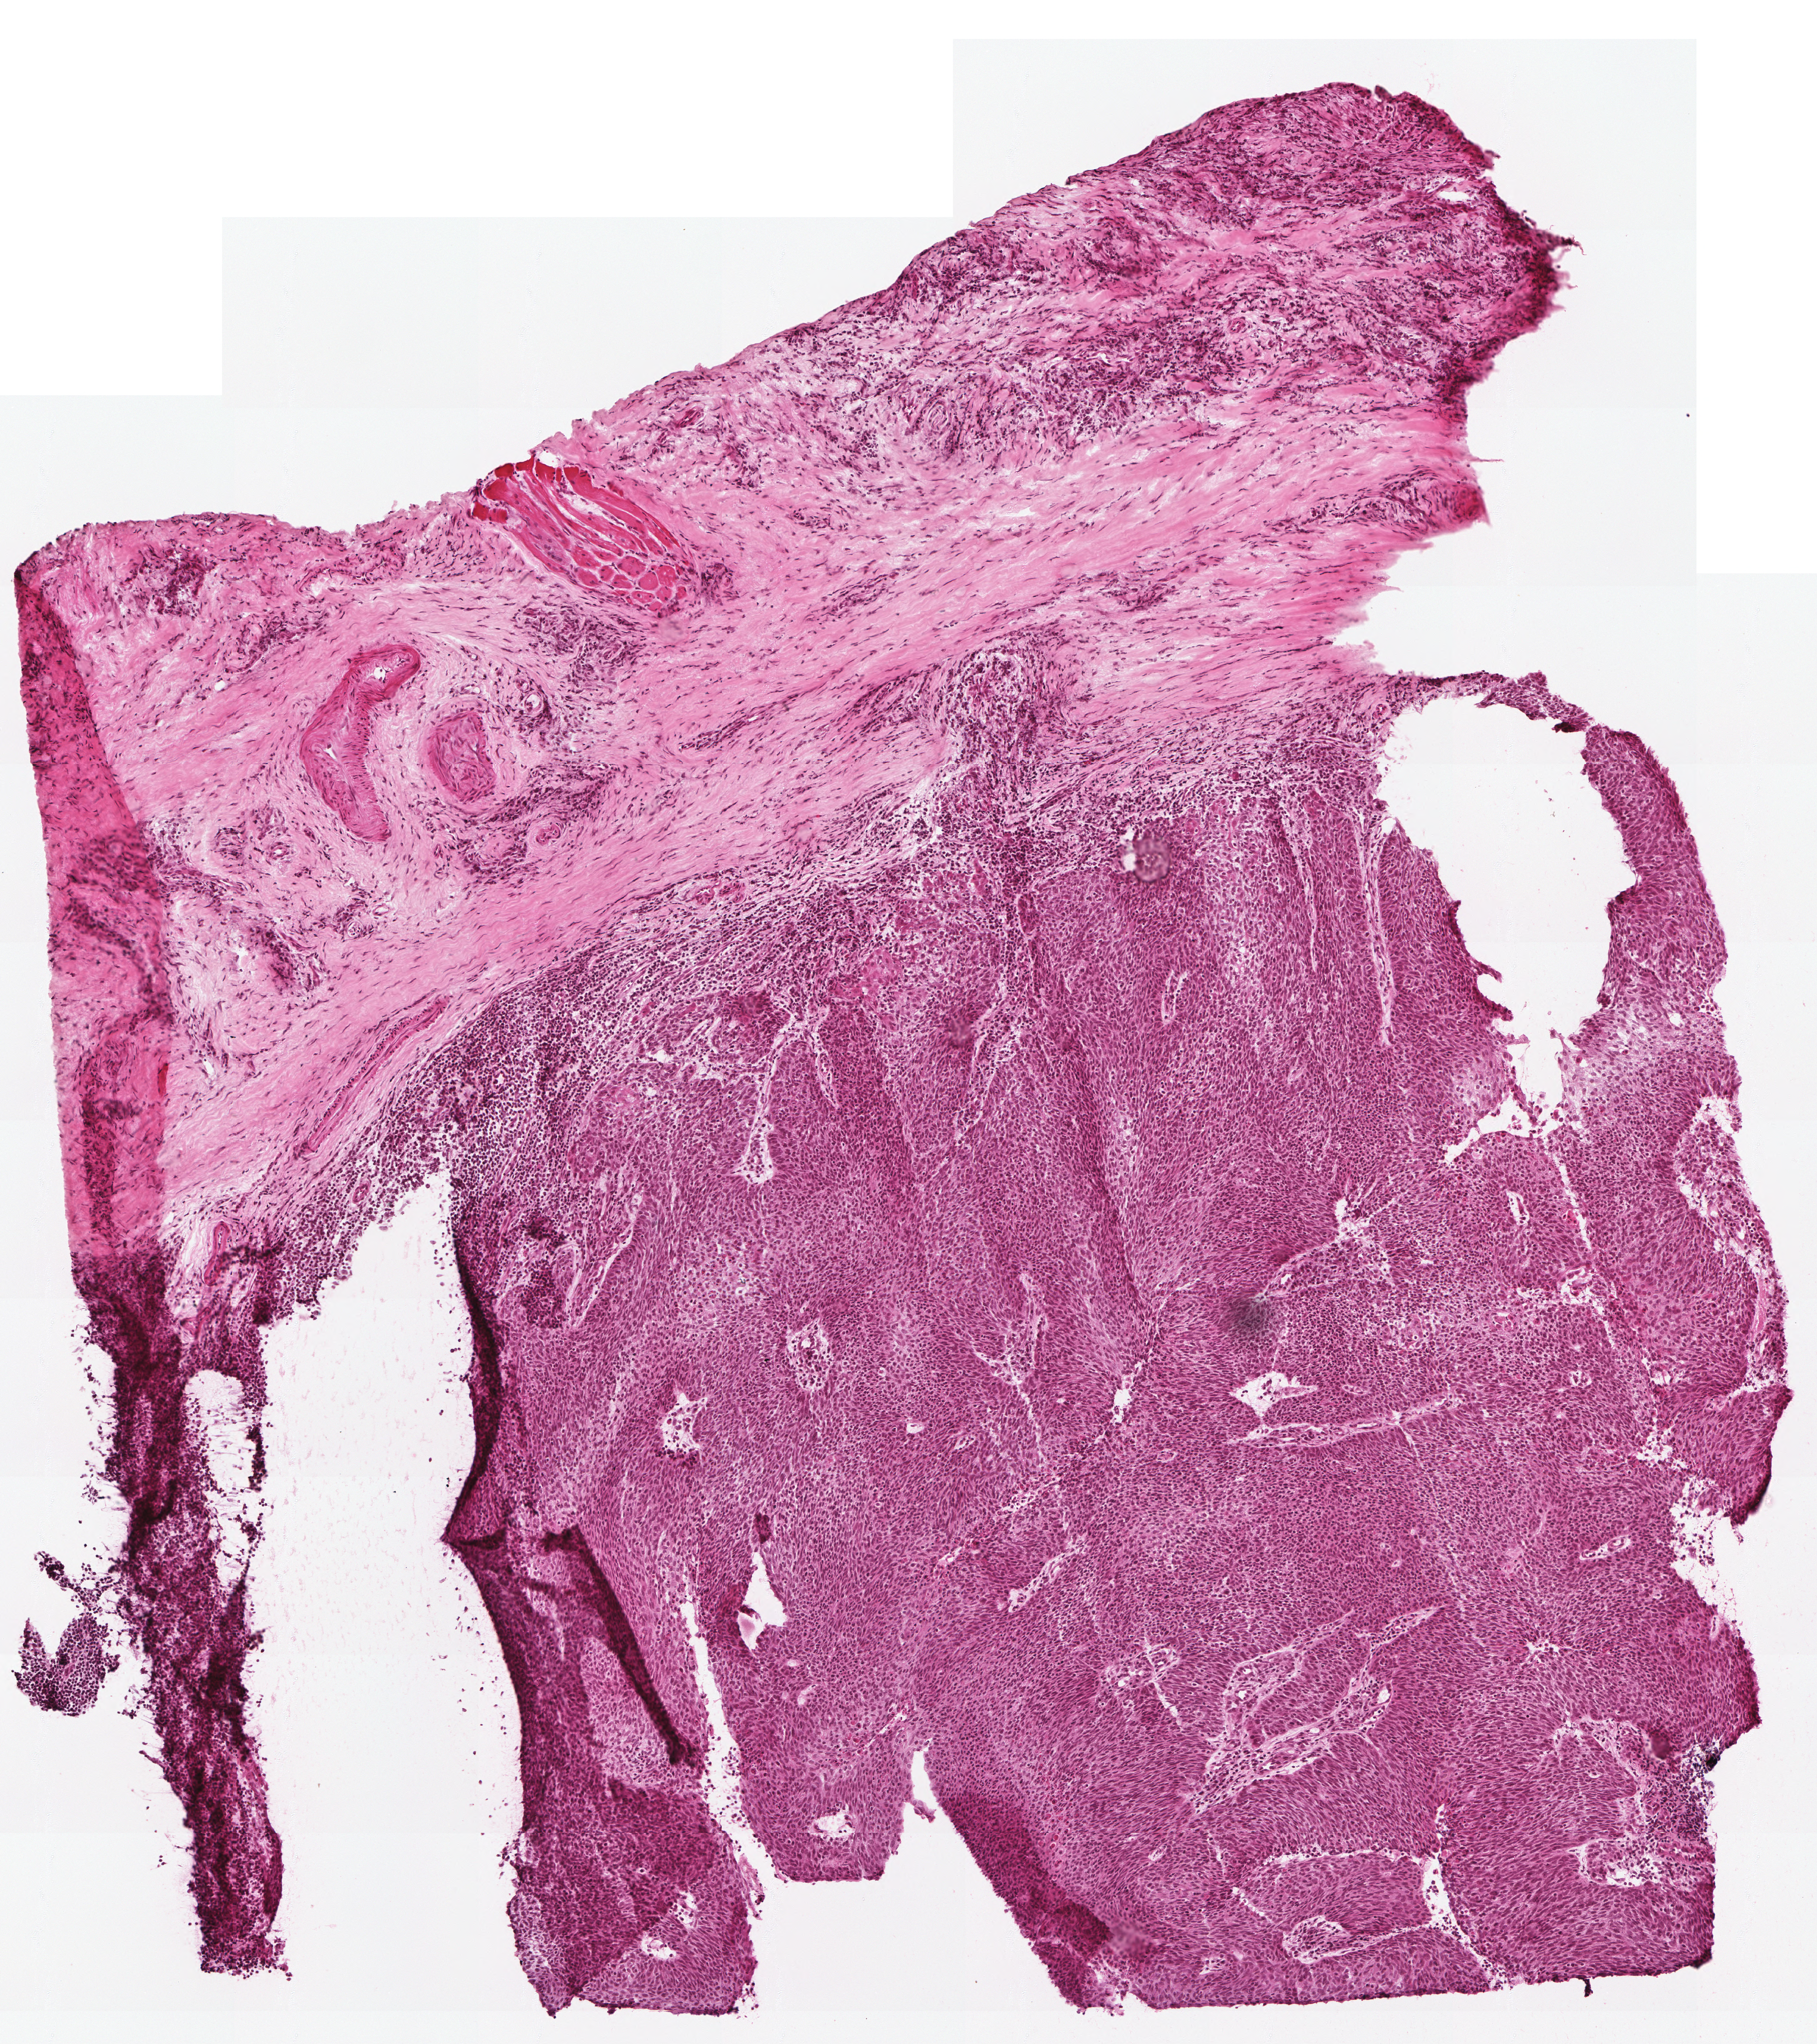
Whole-slide histology image, Hematoxylin and eosin (H&E) stained — the whole scanned area (about 2.6 x 2.9 mm) at the scan's own resolution. Frozen section from the top of the tissue portion. Head and neck, primary tumour sample. Male patient; age at initial diagnosis 38 years. Histologic grade: G2 (moderately differentiated). Pathologist review of this section (percent, as recorded): tumour cells 65%, tumour nuclei 85%, normal cells 0%, stromal cells 35%, necrosis 0%.
AJCC pathologic stage: II. Histologic diagnosis: Squamous cell carcinoma, NOS (tonsil, NOS). Laterality: right.